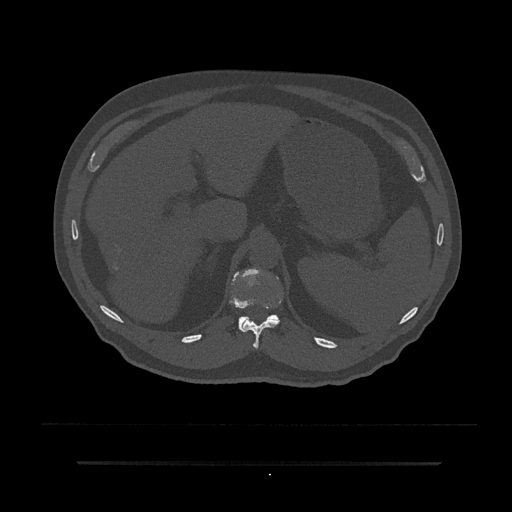
CT including the spine, one axial slice; slice 242 of 797 in the series (ordered by position); reconstruction kernel Br40s/3; 120 kVp; bone window (W 1800 / L 400 HU); 512 × 512 image matrix, field of view 464 × 464 mm. Patient: male, 59 years. From the clinical record (not read from this slice): primary cancer: bile ducts; vertebrae with lytic lesions (as recorded): T10.
Structures marked on this image (semi-automatic segmentation, software-assisted and operator-edited):
- T11 vertebra: bounding box (x1, y1, x2, y2) in pixels: (242, 306, 280, 350)
- T12 vertebra: (230, 269, 280, 332)